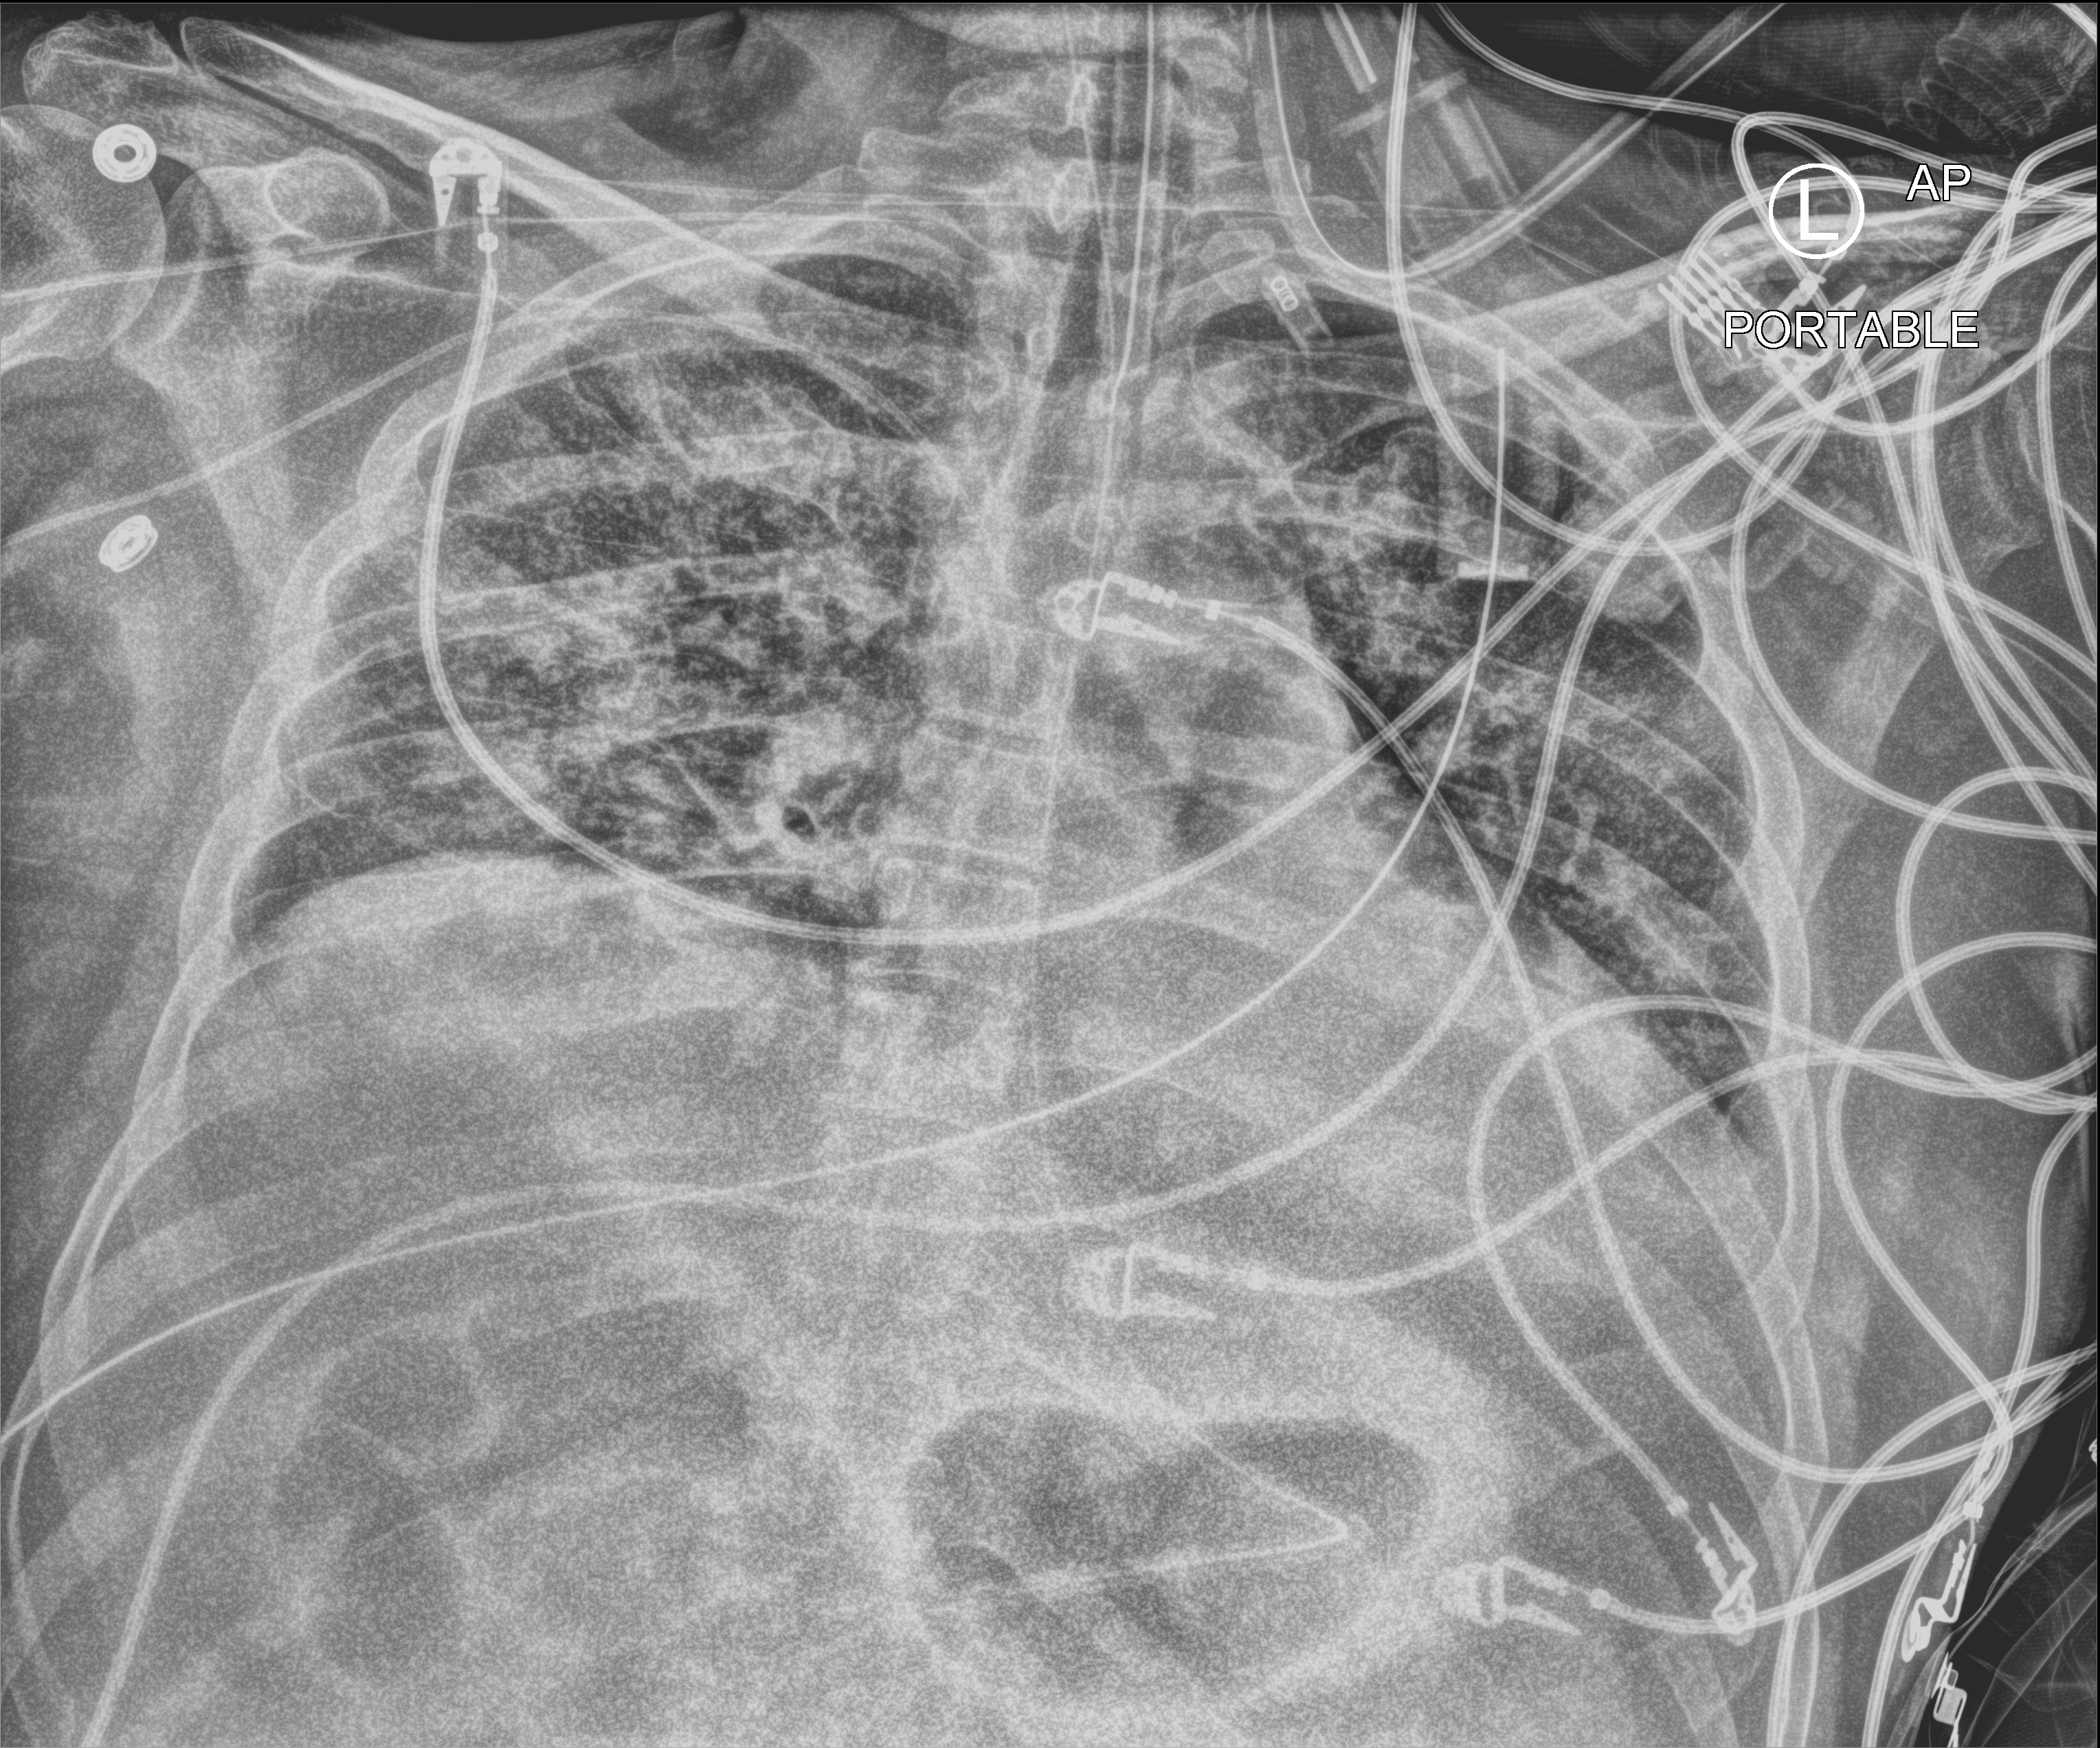
Portable chest radiograph; anteroposterior (AP) projection. Patient hospitalised with COVID-19; male, aged 18–59 years.
Hospital-stay facts (about this admission, not read from this image; timing relative to this image not recorded):
- smoking status (admission record): never
- length of hospital stay: 48 days
- chronic kidney disease (admission record): no